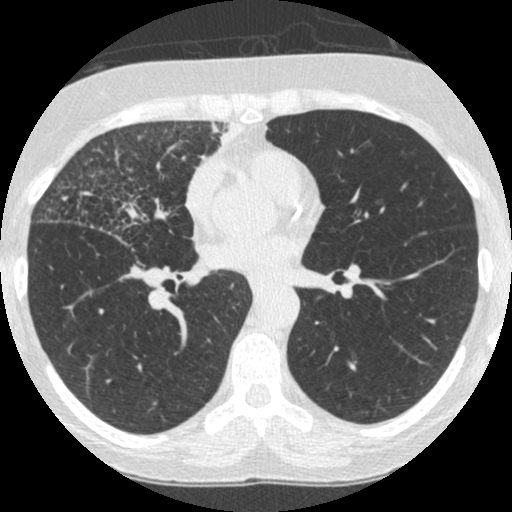
Low-dose screening chest CT, one axial slice. Position 128 of 253 along the scan axis. 120 kVp. Lung window (W 1500 / L -600 HU). 1.25 mm slice thickness. 512 × 512 image matrix.
Structures marked on this image (manually delineated by an expert):
- lesion 4 (tumor, upper lobe of right lung): bounding box [x1, y1, x2, y2] px = [203, 119, 242, 157]